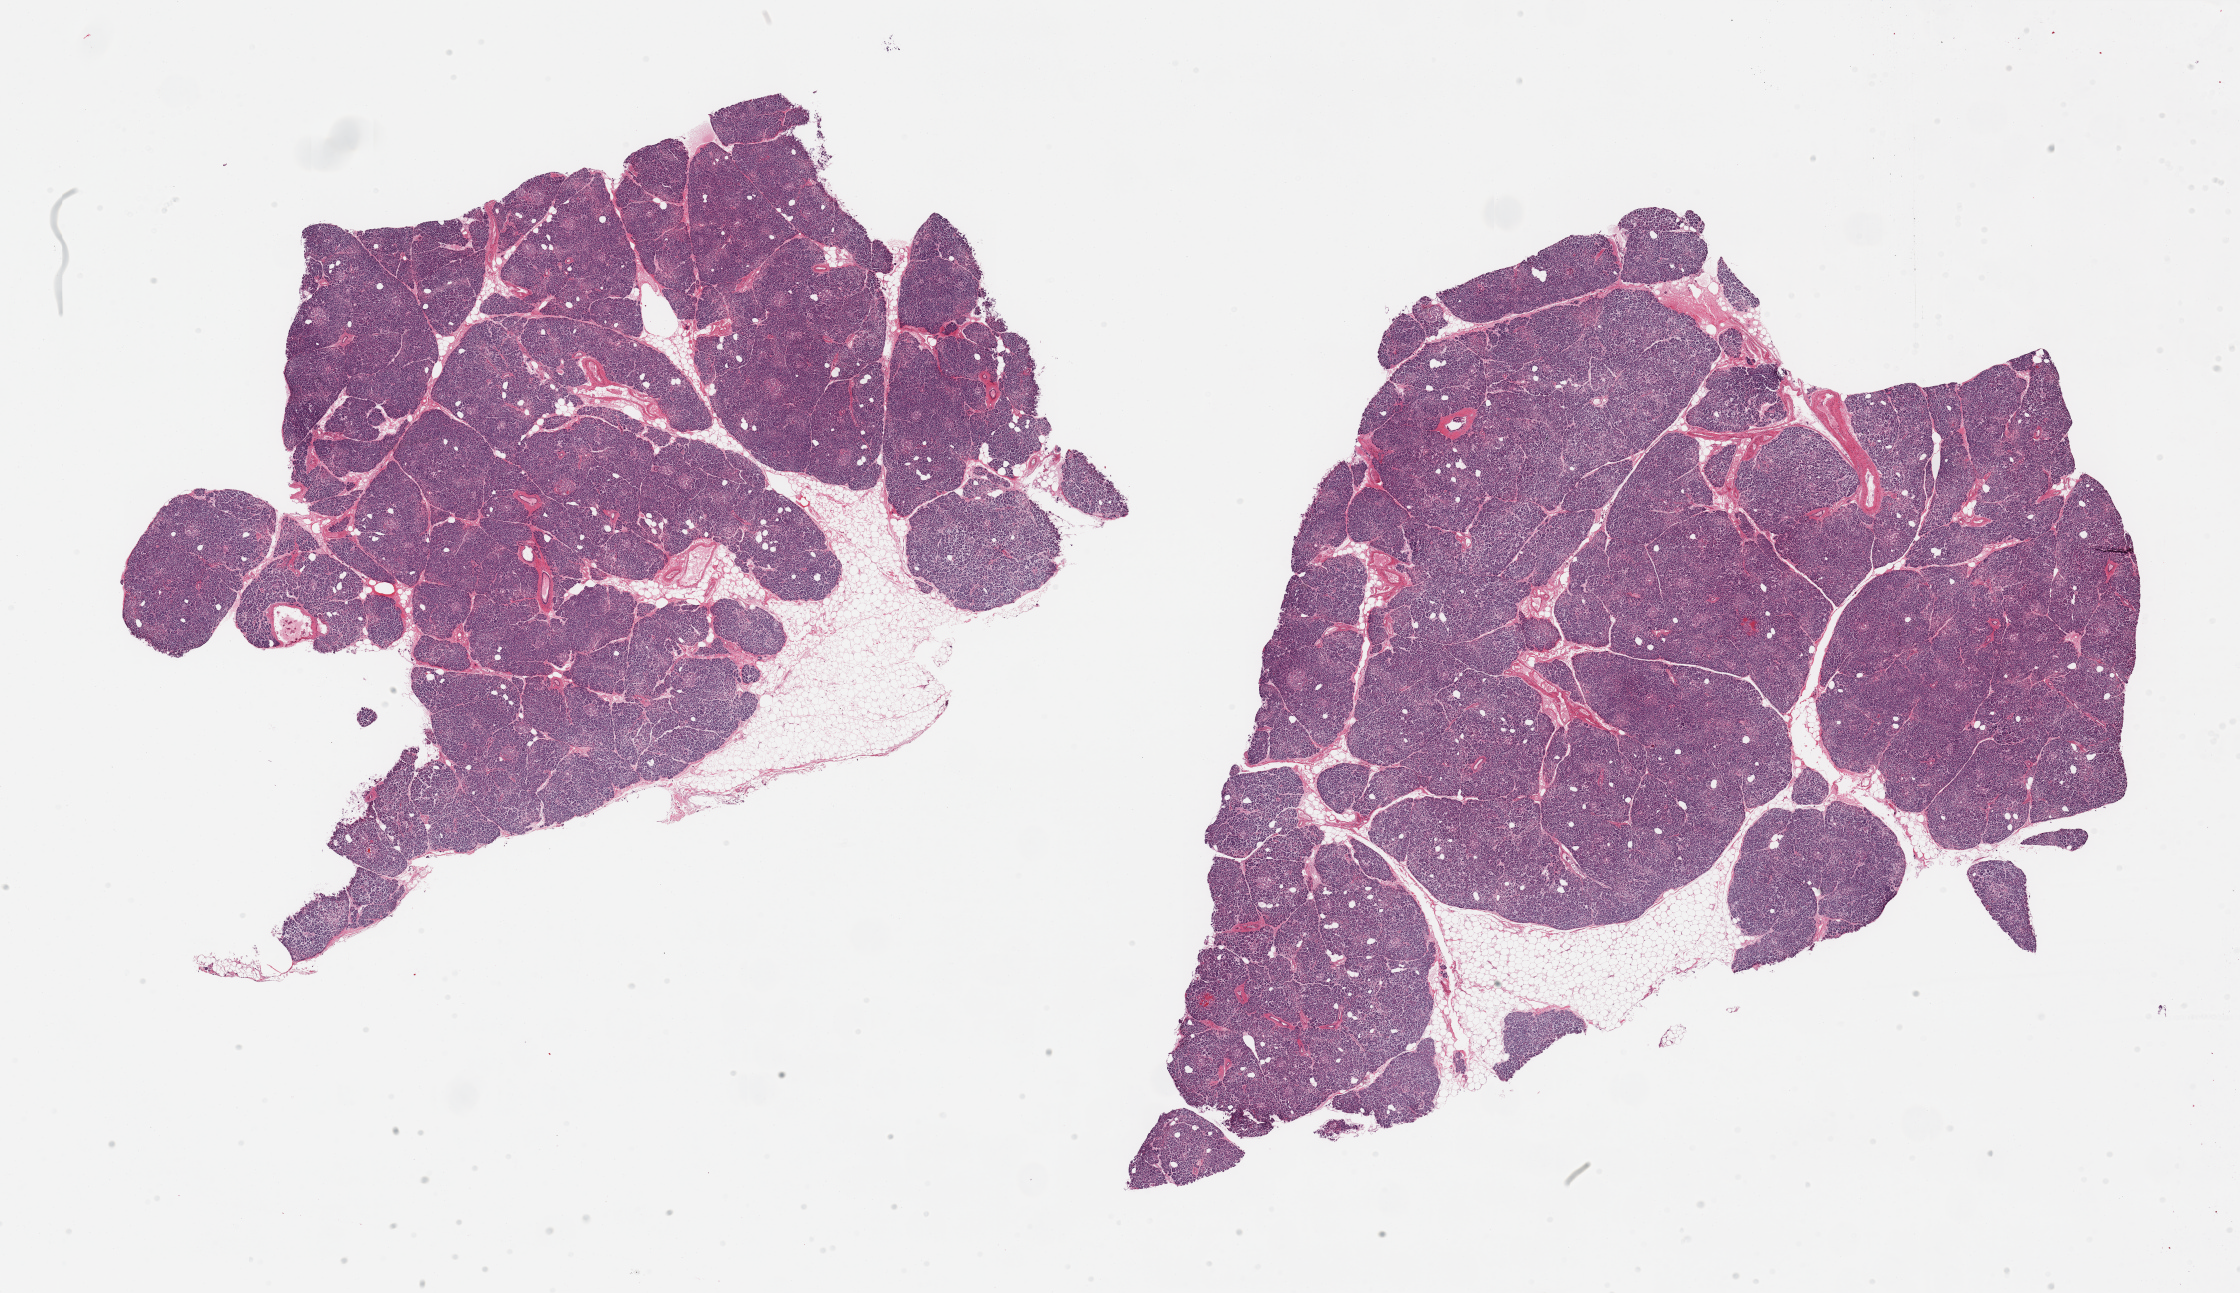
Hematoxylin and eosin (H&E) whole-slide image — low-resolution overview of the scanned area, about 35.4 x 20.5 mm (slide scanned at 20x); PAXgene-fixed, paraffin-embedded tissue; section of pancreas (target tissue); tissue donor sample.
* pathologist's review note for this sample: 2 pieces, some ares approach autolysis score 2 with microfoci of moderately advanced saponification. Islets still well visualized, just beginning to degrade